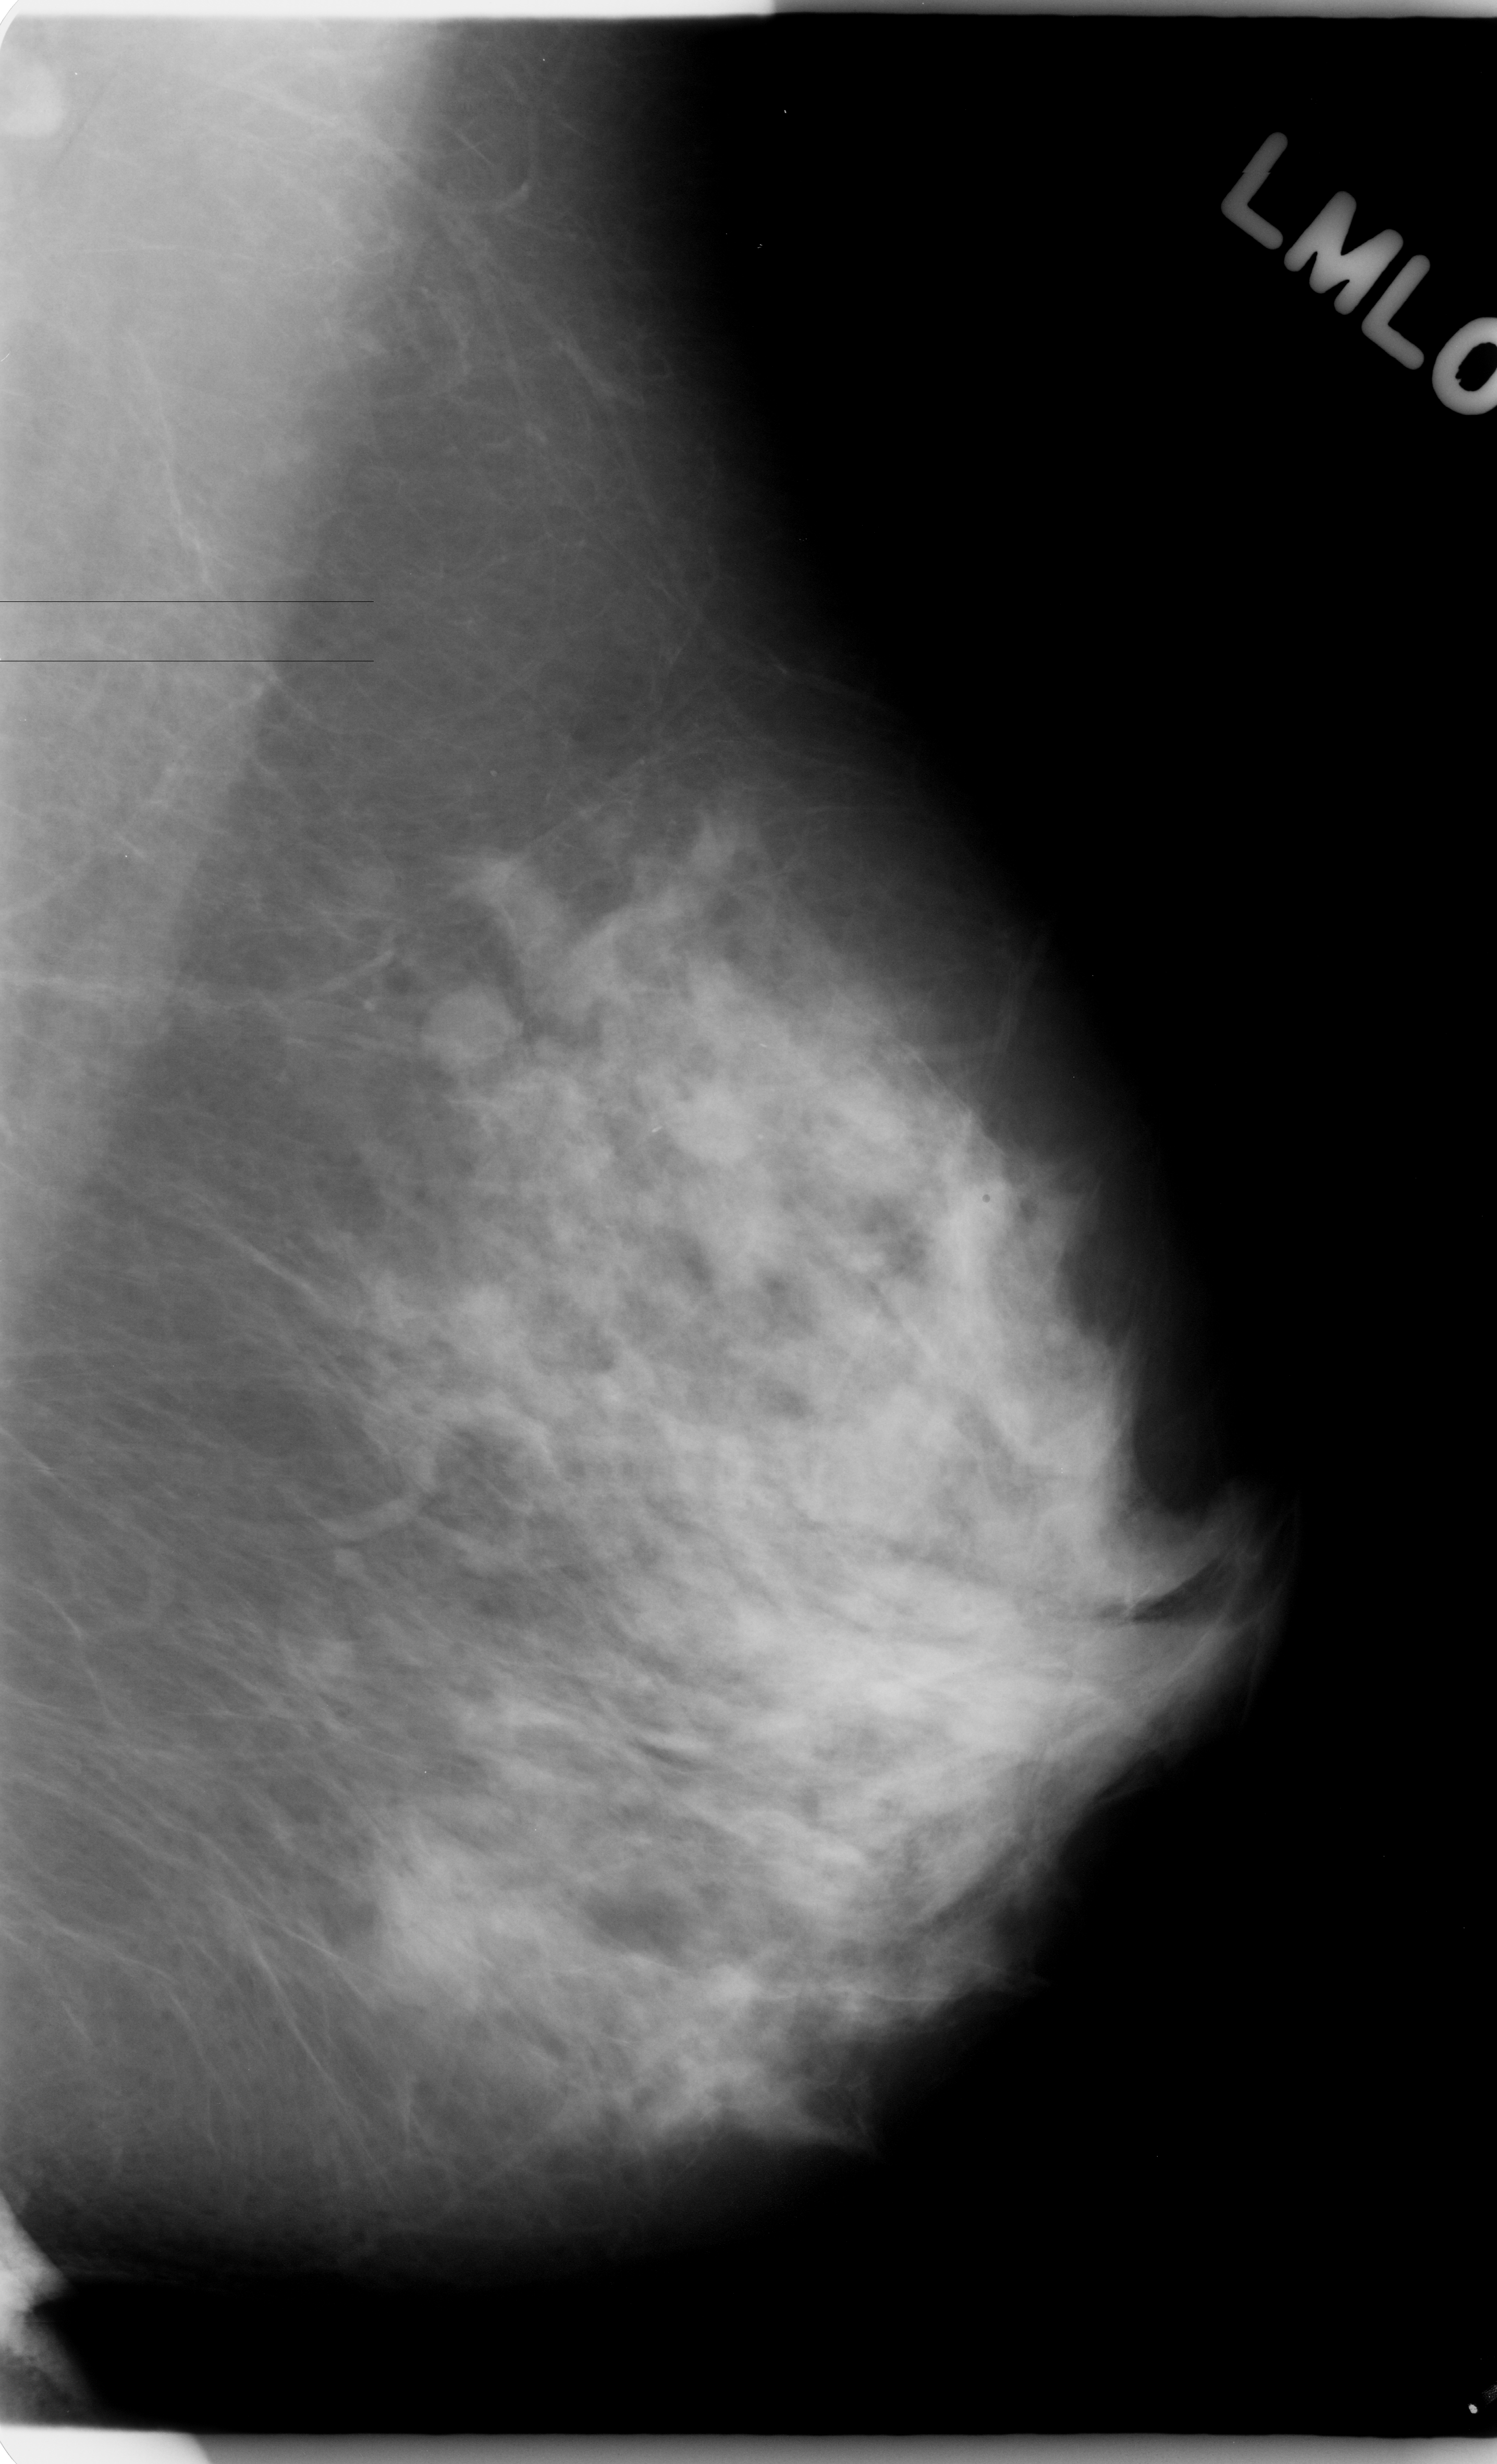
Scanned film-screen mammogram; left breast; MLO view; BI-RADS breast density category 2 (scale 1–4).
- Mass, shape oval, margins circumscribed; BI-RADS assessment category 3; subtlety rating 5 on a 1 (subtle) to 5 (obvious) scale; pathology result (as recorded, not read from the image): benign.